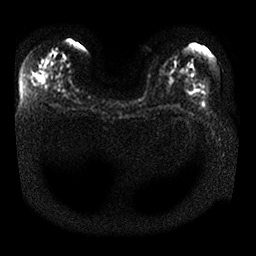
Breast MRI, one axial slice; position 16 of 25 along the scan axis; diffusion-weighted series; image 2 of 4 stored at this slice position (different b-values; order by instance number); 1.5 T; 256 × 256 image matrix, field of view 340 × 340 mm. Female patient.
Outlined on this slice (manually delineated by an expert):
- tumour on diffusion-weighted imaging: bounding box [x1, y1, x2, y2] px = [49, 47, 60, 55]